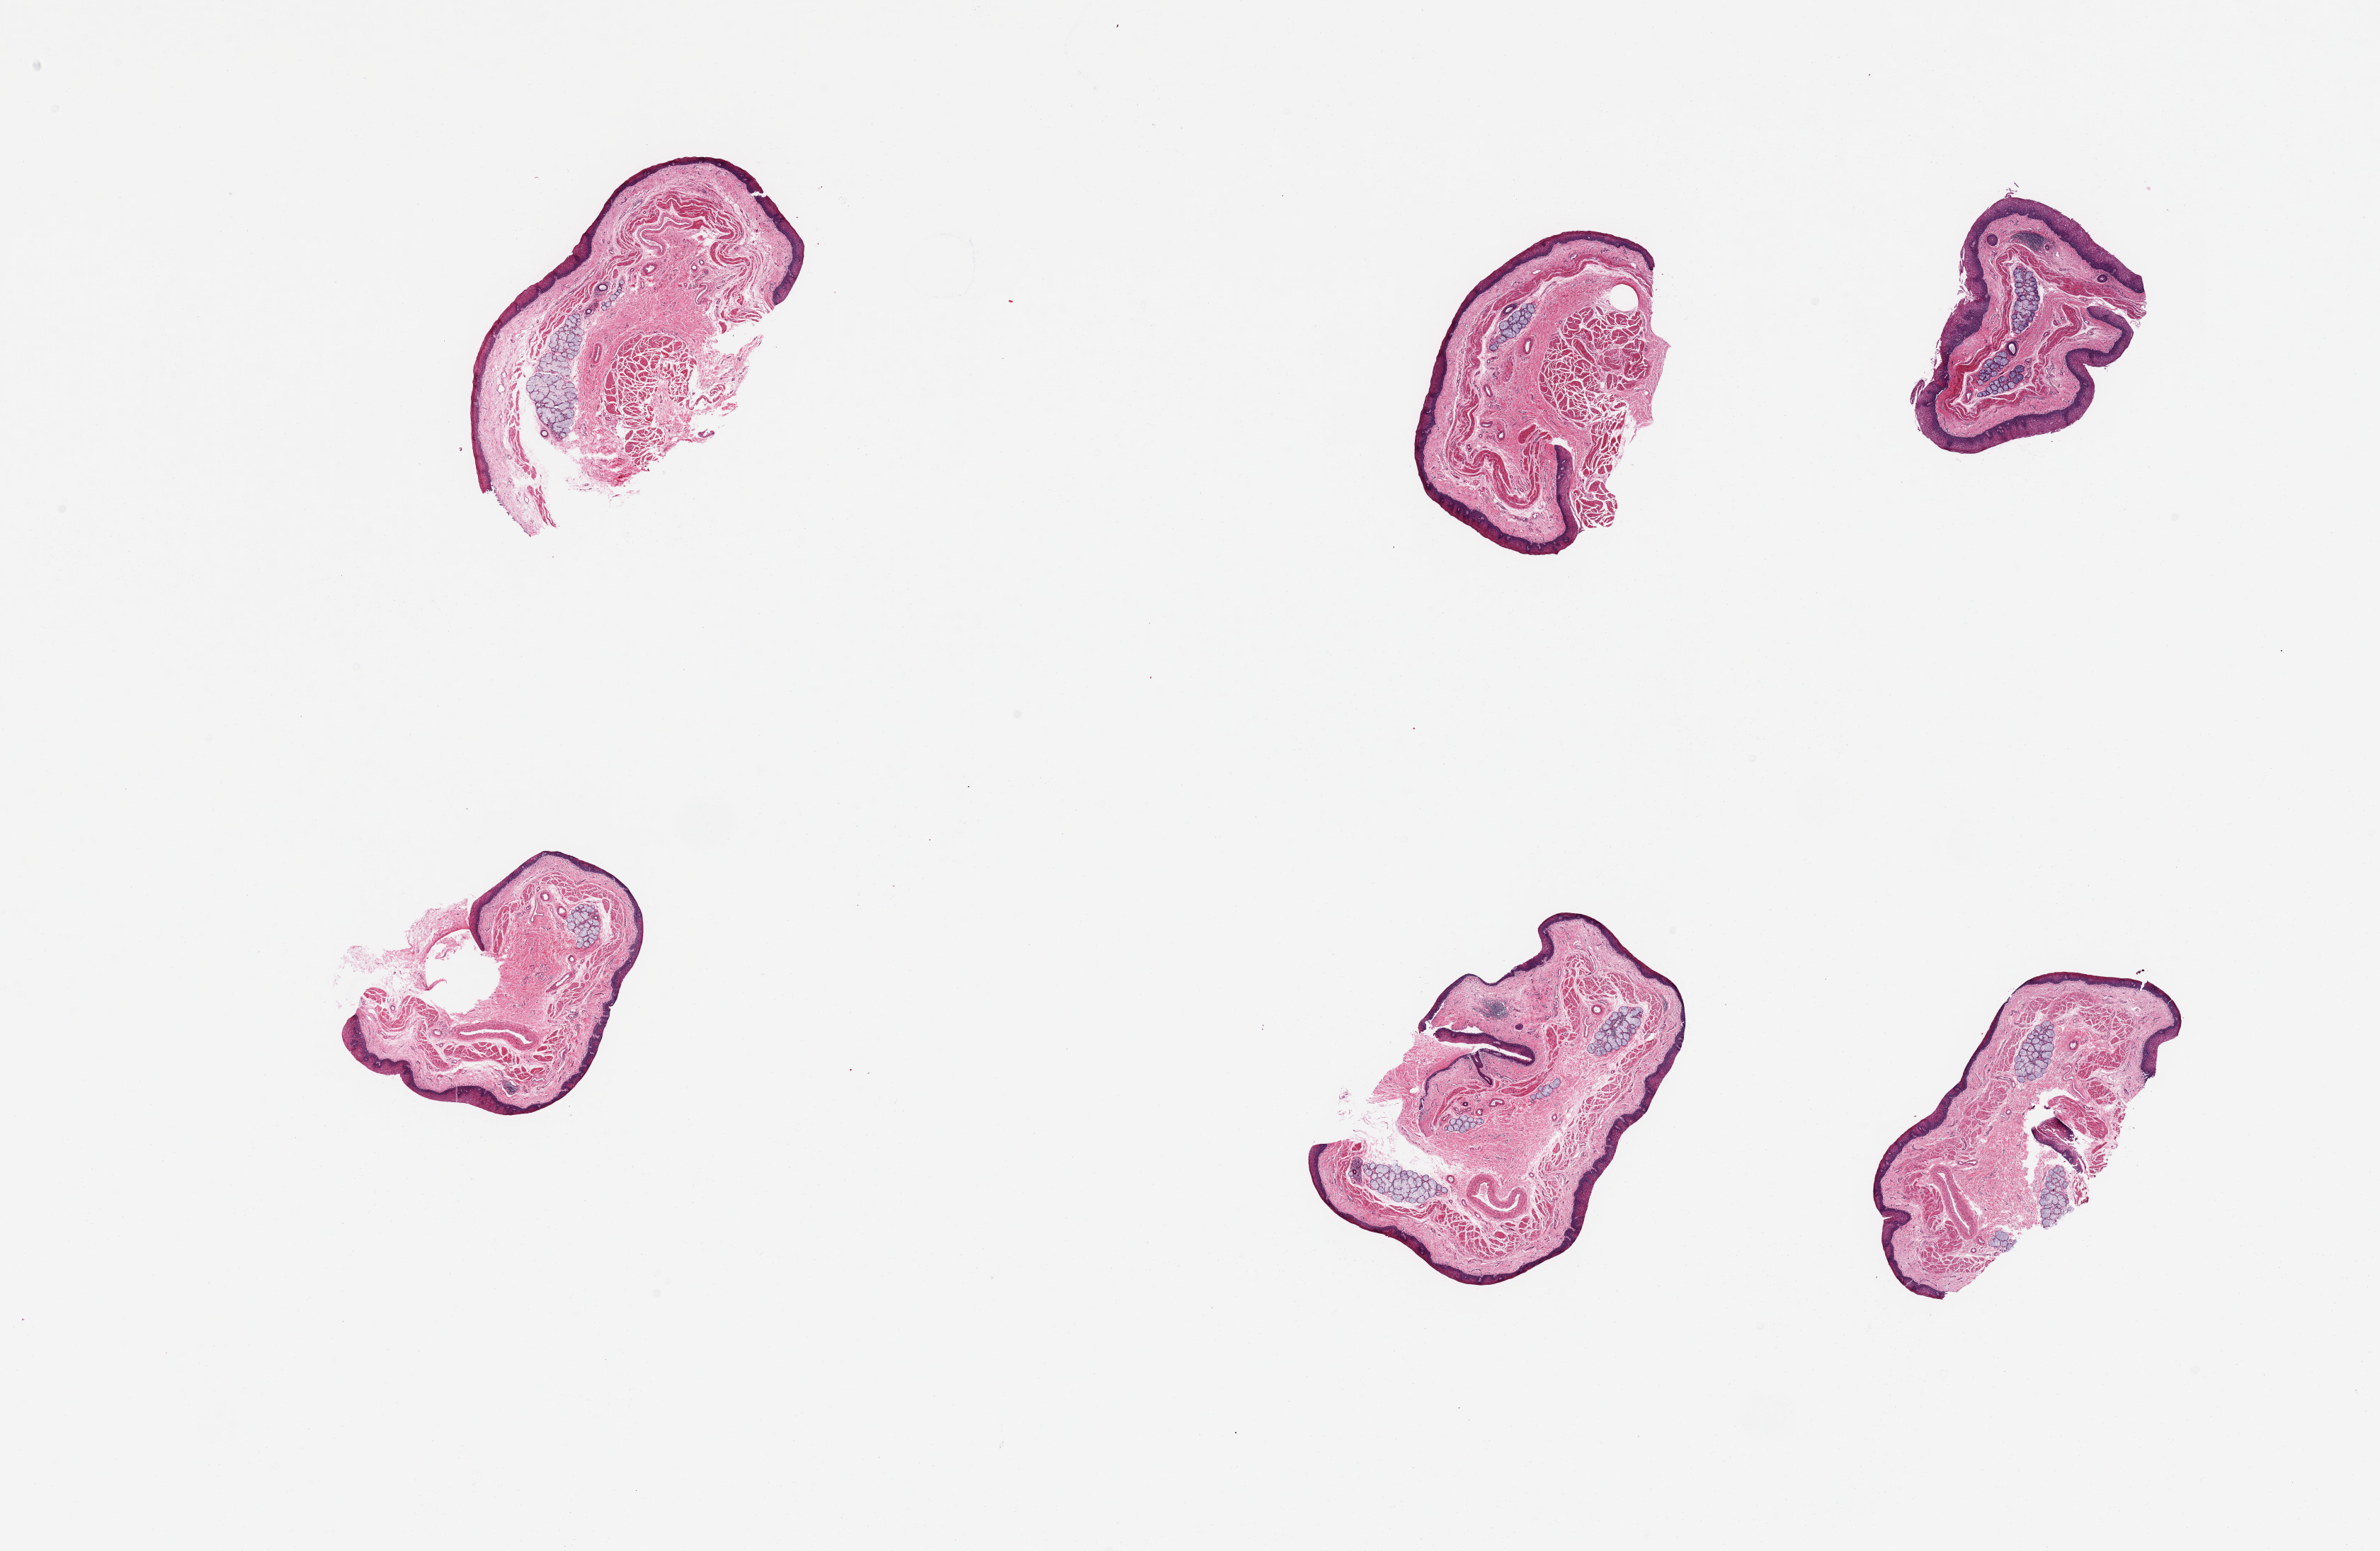
H&E whole-slide image, brightfield, shown as a low-resolution overview of the whole scanned area (about 26.6 x 17.3 mm, acquisition: 20x scan). PAXgene-fixed, paraffin-embedded tissue. Sampled site (target tissue): esophageal mucous membrane. Tissue donor sample. Female donor.
• reviewer comment on this tissue sample: 6 pieces, squamous mucosa is ~0.2mm, ~10% of thickness, prominent submucosal mucus gland present